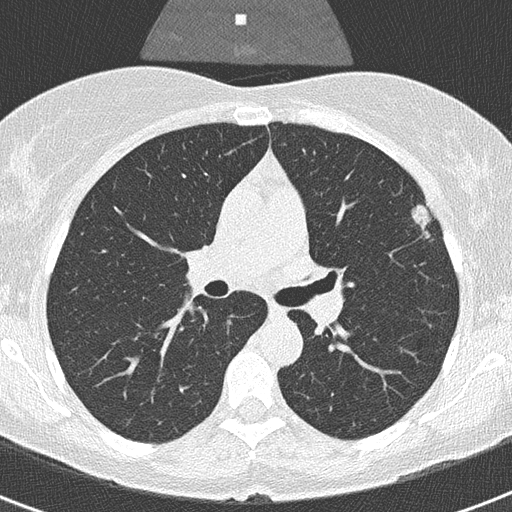
Low-dose screening chest CT, axial slice. Second screening round (one year after baseline). Lung window (W 1500 / L -600 HU). 2 mm slice thickness. Lung (sharp) reconstruction kernel (B50f). Female participant, aged 56 years at enrolment.
Lesion marked by an expert reader, bounding box <407,201,455,254> (left, top, right, bottom; pixels). Reader record for this screening exam (exam-level; its link to the box is not recorded): non-calcified nodule or mass ≥4 mm, left upper lobe, 20 × 9 mm, smooth margins, soft tissue attenuation, pre-existing on the prior screen: yes; interval growth: yes. Official screen result: positive, other.